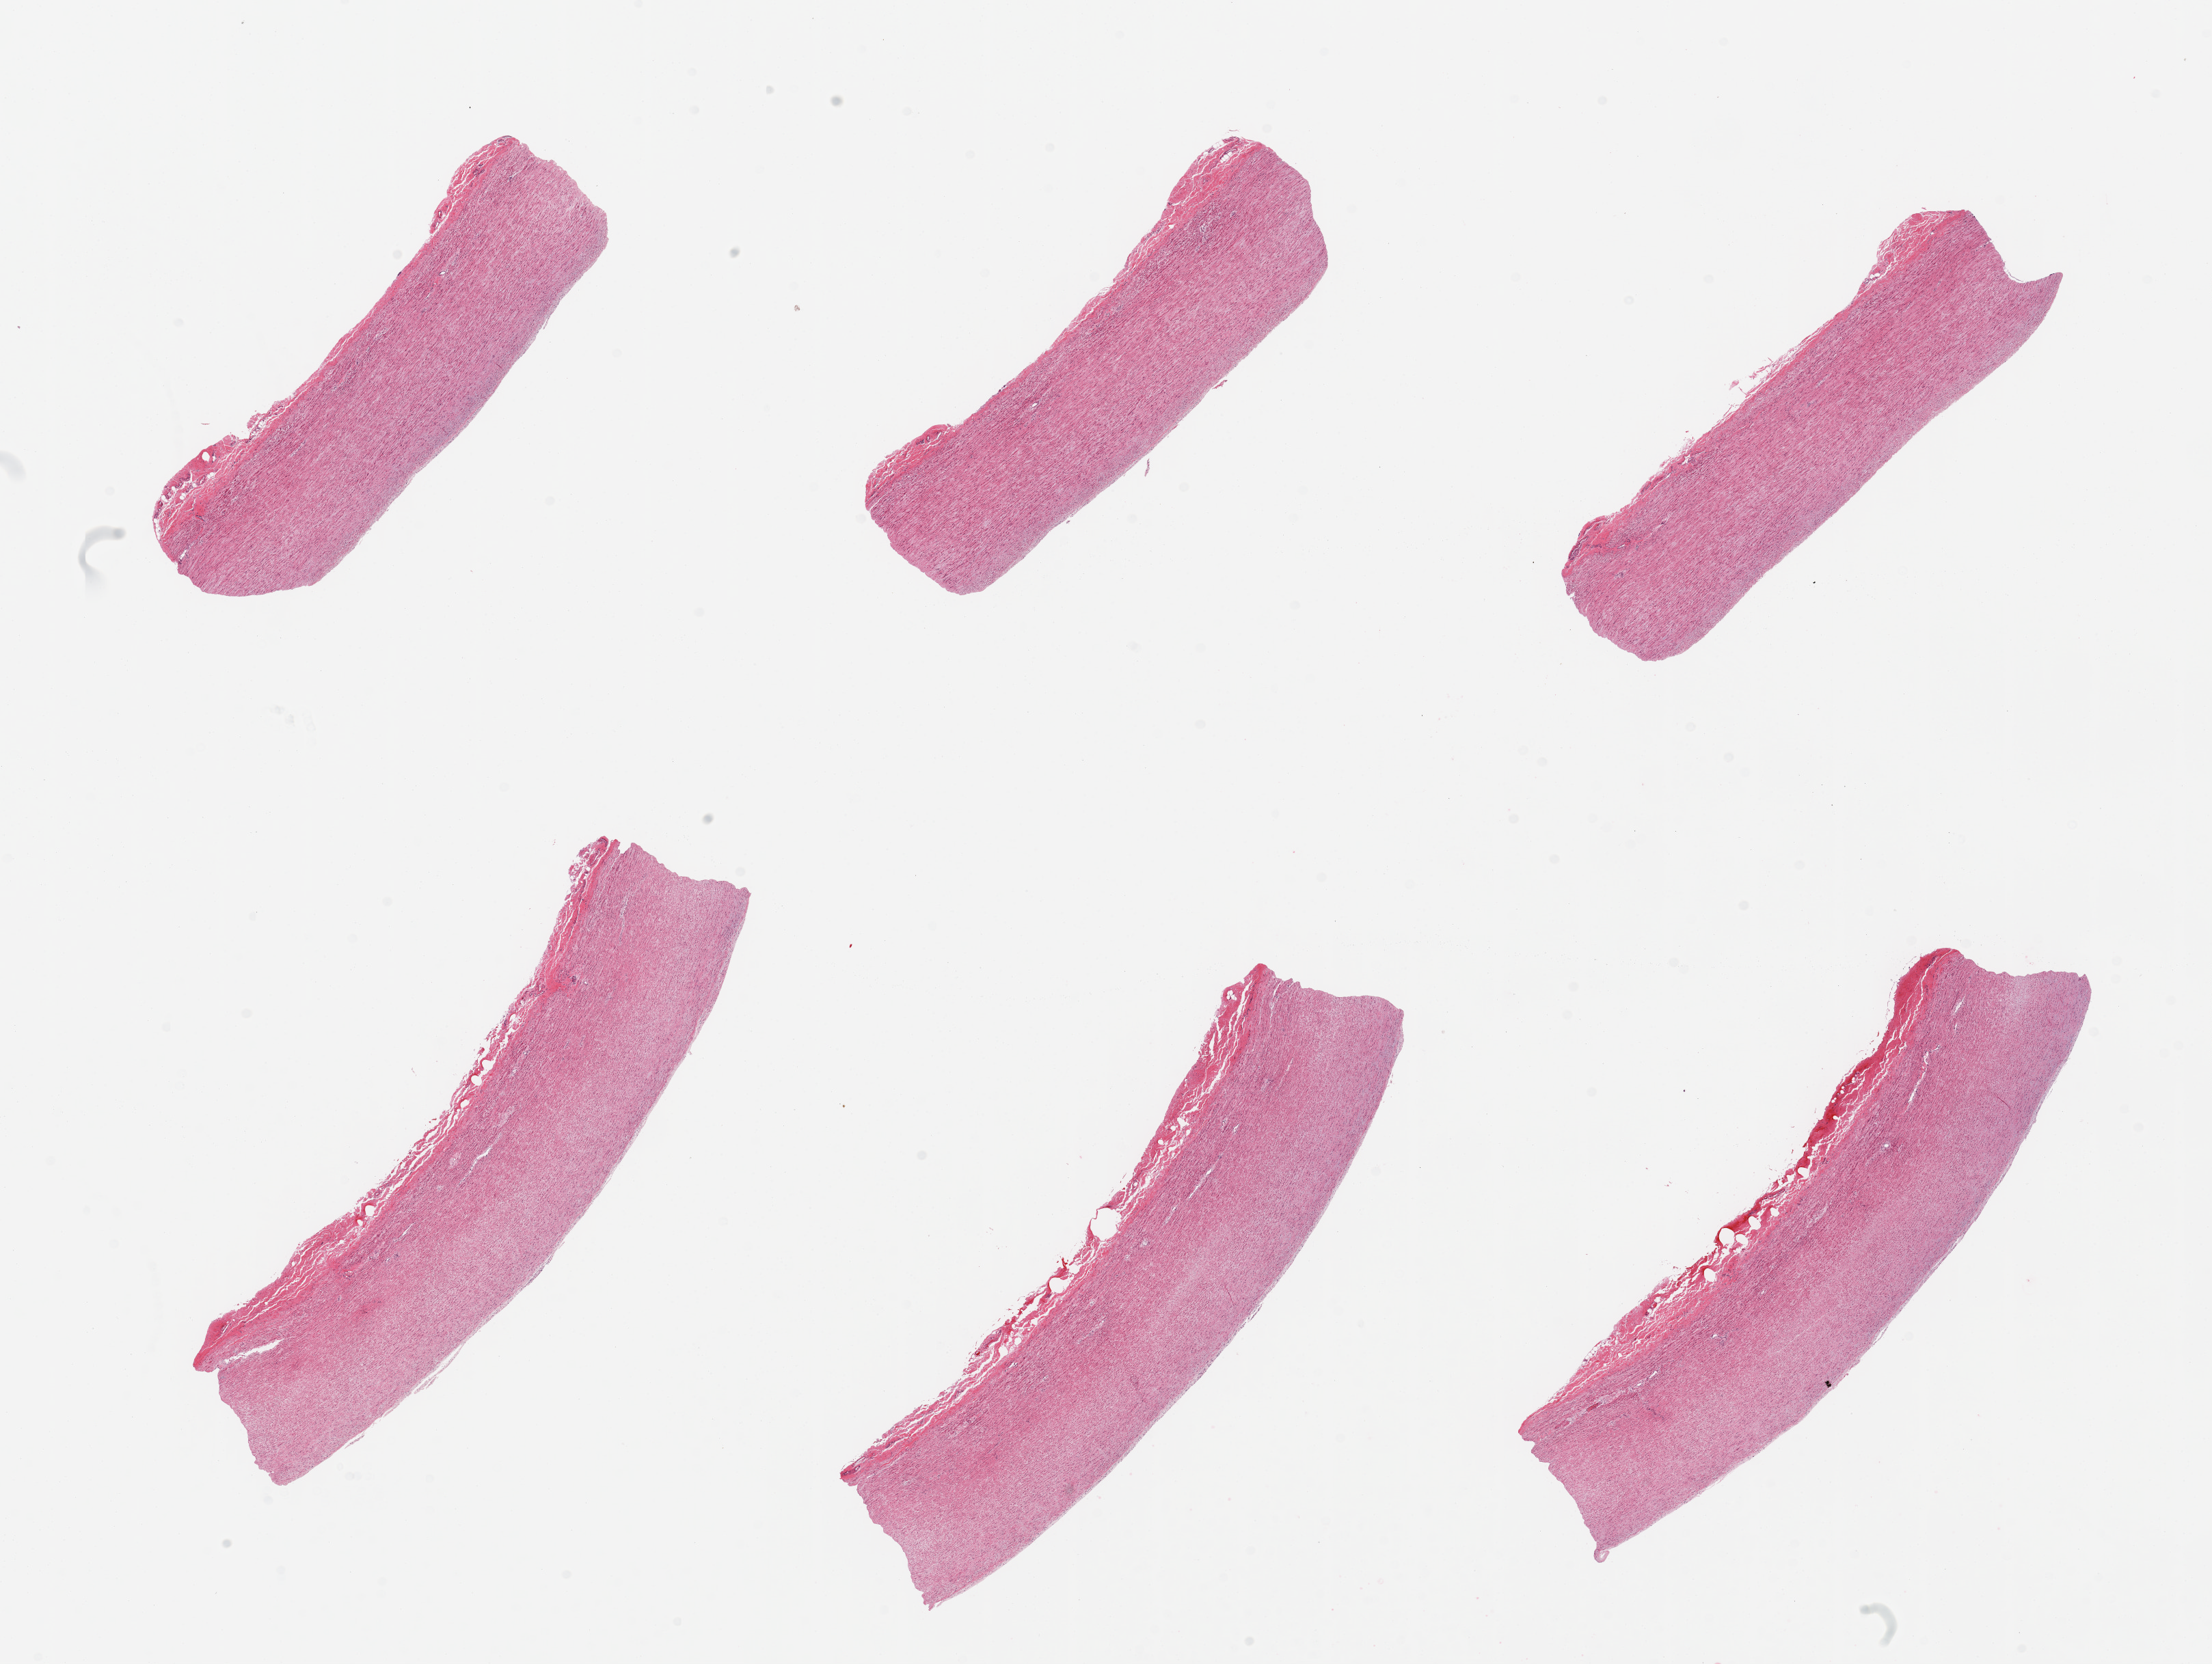
Whole-slide image, H&E stain — whole scanned area (about 25.6 x 19.3 mm) shown as a low-resolution overview, PAXgene-fixed paraffin-embedded (PFPE) section, sampled site (target tissue): aorta, donor tissue sample. Donor sex: female.
Reviewer comment on this tissue sample: 6 pieces, minimal atherosis.